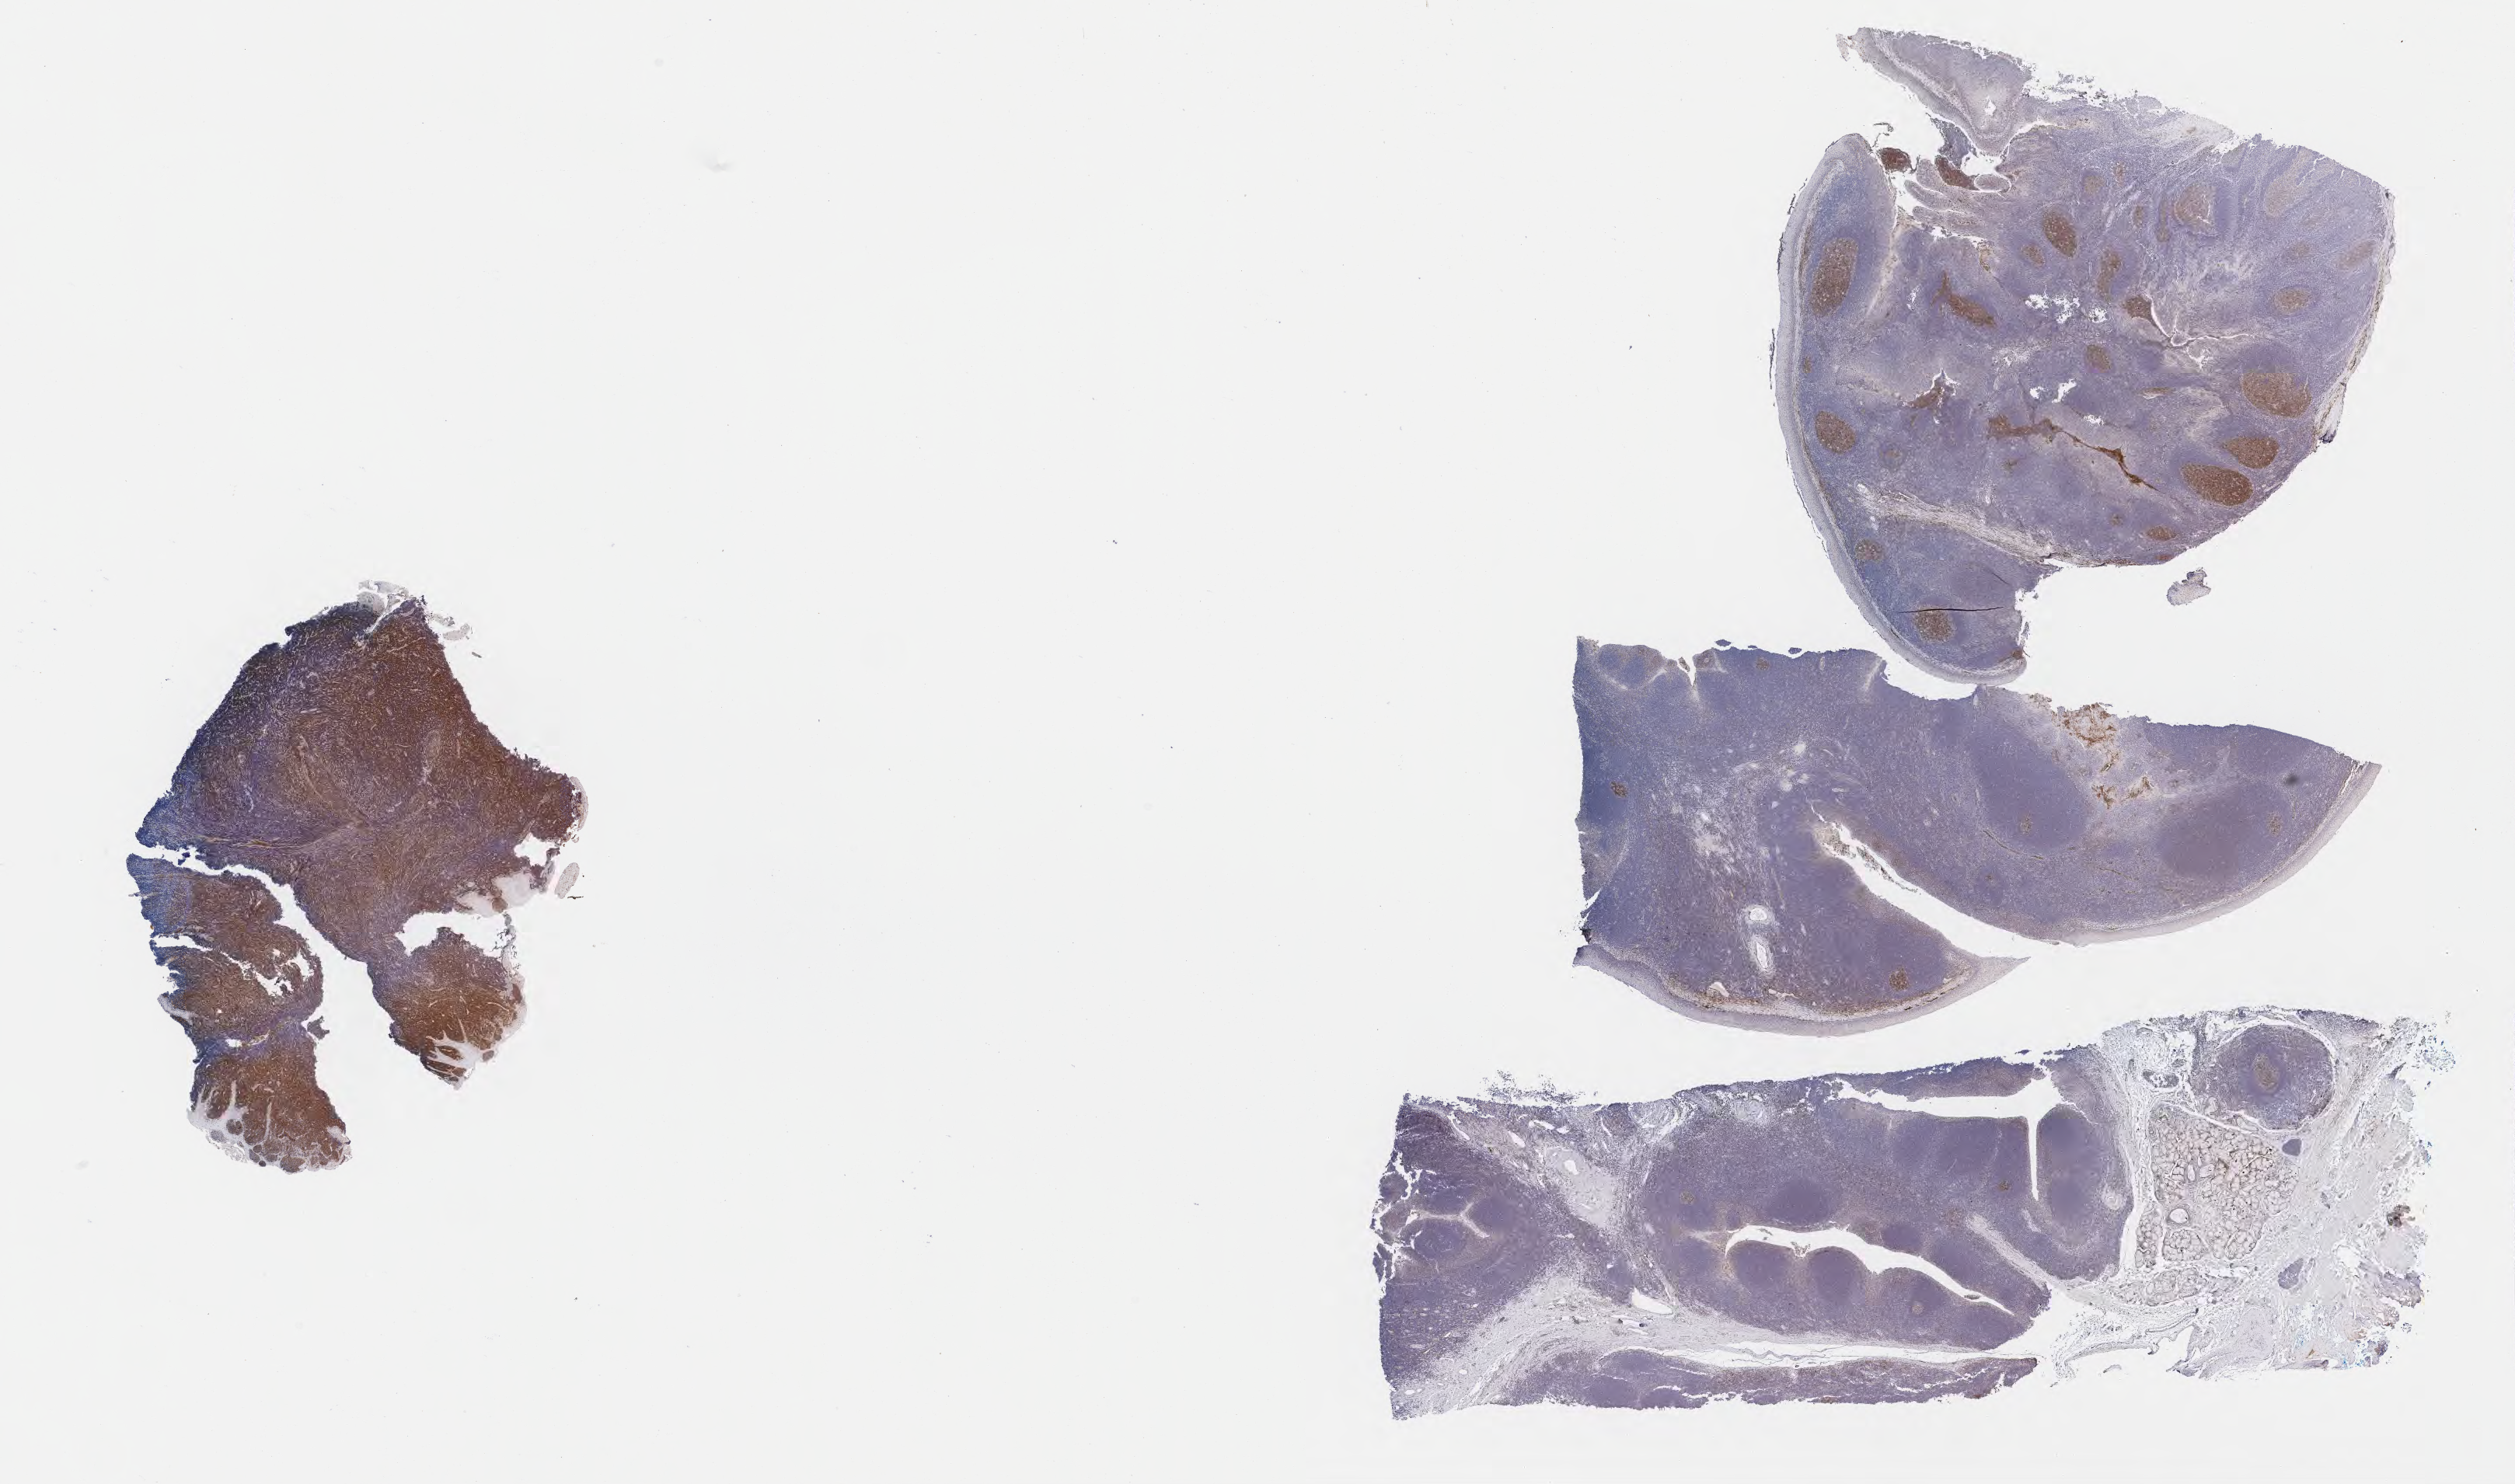
IHC for CD10, whole-slide image, a low-resolution overview of the entire scanned area, about 26.2 x 15.4 mm, tumor tissue, site: cranium. Patient male; age 11 years.
Diagnosis: Diffuse large B-cell lymphoma, NOS.